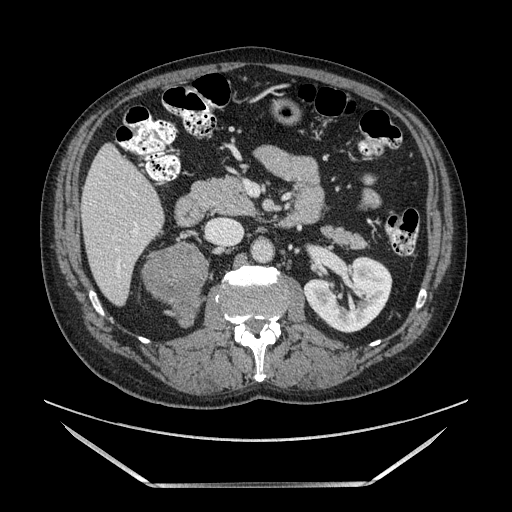
Contrast-enhanced abdominal CT, one axial slice; slice 55 of 185 in the series (ordered by position); soft-tissue window (W 400 / L 40 HU); 1.25 mm slice thickness; 512 × 512 image matrix, field of view 440 × 440 mm. Male patient. From the clinical record (not read from this slice): diagnosis: adrenocortical carcinoma; tumour side: right adrenal; tumour size at pathology: 10.3 cm; Ki-67 index: 20 %; stage (as recorded): 3.
Structures marked on this image (semi-automatically segmented with operator editing):
- mass: bounding box (x1, y1, x2, y2) in pixels: (144, 242, 206, 326)